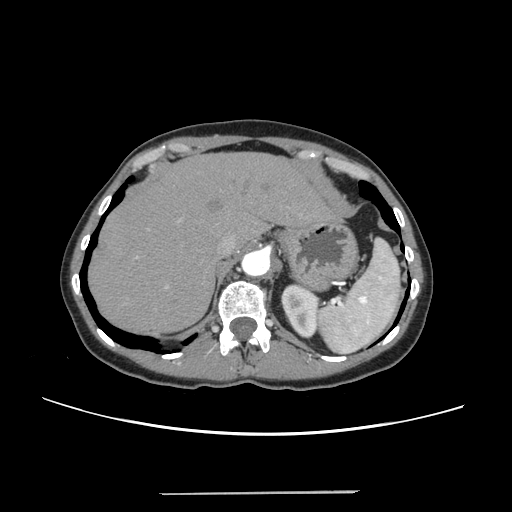
Contrast-enhanced abdominal CT, one axial slice. Slice 190 of 240 in the series (ordered by position). 120 kVp. Intravenous contrast given. Soft-tissue window (W 400 / L 40 HU). 1.25 mm slice thickness. 512 × 512 image matrix. Female patient, age 60 years. From the clinical record (not read from this slice): diagnosis: colorectal cancer liver metastases, imaged before liver resection; multiple liver metastases: no; largest metastasis: 1.5 cm; disease in both lobes: no.
Structures marked on this image (outlined manually by an expert reader):
- hepatic veins: box from (x=217, y=236) to (x=235, y=254) px
- liver: (x=89, y=154)–(x=334, y=334)
- planned liver remnant (the part of the liver to remain after resection): (x=89, y=154)–(x=334, y=334)
- portal vein (with intrahepatic branches): (x=166, y=218)–(x=180, y=288)